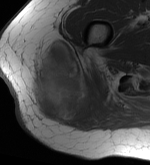
MRI of an extremity soft-tissue mass, one axial slice. Slice 17 of 56 in the series (ordered by position). MR volume resampled by the dataset authors to the PET/CT grid (not the native acquisition matrix). 3.27 mm slice thickness. 150 × 165 image matrix, field of view 146 × 161 mm. Female patient. Case-level facts recorded for this patient, not image findings: histological type: epithelioid sarcoma with vascular differentiation; site of the primary tumour: right buttock.
Structures marked on this image (expert contour drawn on MRI and transferred to this co-registered scan by the dataset authors):
- gross tumour volume (mass): bounding box [x1, y1, x2, y2] px = [30, 40, 108, 125]